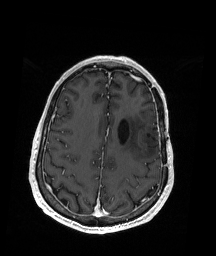
Brain MRI from a brain-tumour surgery series, one axial slice; slice 61 of 192 in the series (ordered by position); T1-weighted post-contrast; 1 mm slice thickness; 216 × 256 image matrix, field of view 211 × 250 mm. Case-level facts recorded for this patient, not image findings: histopathology: Oligodendroglioma; WHO grade: 2; IDH mutation: yes.
Annotated regions visible in this slice (manually delineated by an expert):
- previous resection cavity: bounding box [x1, y1, x2, y2] px = [132, 124, 163, 139]